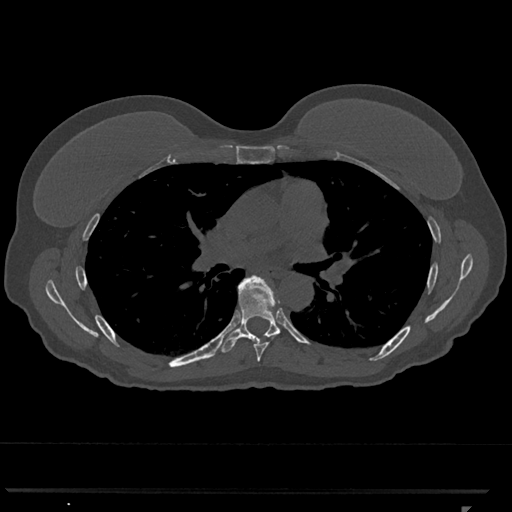
CT including the spine, one axial slice. Slice 735 of 793 in the series (ordered by position). Reconstruction kernel Br40s/3. Bone window (W 1800 / L 400 HU). 512 × 512 image matrix, field of view 380 × 380 mm. Patient: female, 62 years. From the clinical record (not read from this slice): primary cancer: renal.
Structures marked on this image (semi-automatic segmentation, software-assisted and operator-edited):
- T6 vertebra: bounding box [x1, y1, x2, y2] px = [254, 285, 271, 362]
- T7 vertebra: [217, 275, 281, 353]